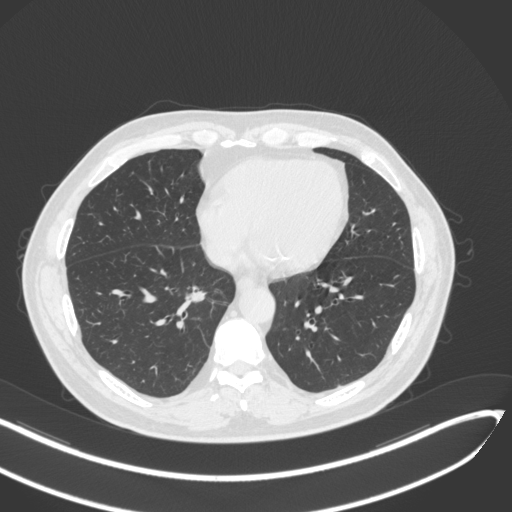
Chest CT, one axial slice. Slice 136 of 429 in the series (ordered by position). 120 kVp. Lung window (W 1500 / L -600 HU). 512 × 512 image matrix, field of view 400 × 400 mm. Patient: male, 62 years. From the clinical record (not read from this slice): clinical TNM (as recorded): T1b N0 M0.
Structures marked on this image (rectangle marked by the reading radiologist):
- lung tumour (recorded histology: adenocarcinoma): bounding box (x1, y1, x2, y2) in pixels: (177, 282, 211, 314)